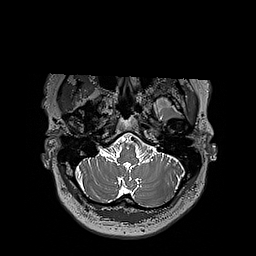
Brain MRI from a brain-tumour surgery series, one axial slice. Position 159 of 192 along the scan axis. 1 mm slice thickness. 256 × 256 image matrix. Case-level facts recorded for this patient, not image findings: histopathology: Oligodendroglioma; WHO grade: 3; IDH mutation: yes.
Annotated regions visible in this slice (expert manual segmentation):
- tumour: box from (x=124, y=96) to (x=197, y=109) px